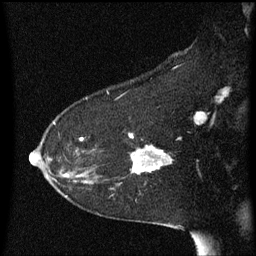
Breast MRI (dynamic contrast-enhanced), one sagittal slice. Slice 40 of 60 in the series (ordered by position). Dynamic contrast-enhanced series, image 2 of 3 at this slice position (ordered by acquisition). 1.5 T. TE 4.2 ms, TR 8.4 ms. 2 mm slice thickness. 256 × 256 image matrix, field of view 200 × 200 mm. Female patient, age 54 years. Case-level facts recorded for this patient, not image findings: setting: breast cancer imaged before/during neoadjuvant chemotherapy; receptor status: HR-positive, HER2-negative.
Outlined on this slice (semi-automatic segmentation, software-assisted and operator-edited):
- analysis volume of interest (the breast-tissue region the enhancement analysis was run in; not a lesion): bounding box (x1, y1, x2, y2) in pixels: (121, 134, 175, 185)
- tumour enhancement mask (voxels above the 70 % enhancement threshold inside the analysis volume of interest): (132, 146, 164, 173)